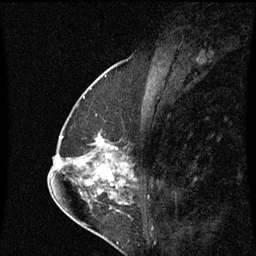
Breast MRI (dynamic contrast-enhanced), one sagittal slice; position 32 of 60 along the scan axis; dynamic contrast-enhanced series, image 2 of 3 at this slice position (ordered by acquisition); 1.5 T; TE 4.2 ms, TR 8.9 ms; 2 mm slice thickness; 256 × 256 image matrix. Patient: female, 57 years. Case-level facts recorded for this patient, not image findings: setting: breast cancer imaged before/during neoadjuvant chemotherapy; receptor status: HR-positive, HER2-negative.
Outlined on this slice (semi-automatically segmented with operator editing):
- analysis volume of interest (the breast-tissue region the enhancement analysis was run in; not a lesion): bounding box (x1, y1, x2, y2) in pixels: (83, 134, 115, 159)
- tumour enhancement mask (voxels above the 70 % enhancement threshold inside the analysis volume of interest): (99, 138, 111, 159)